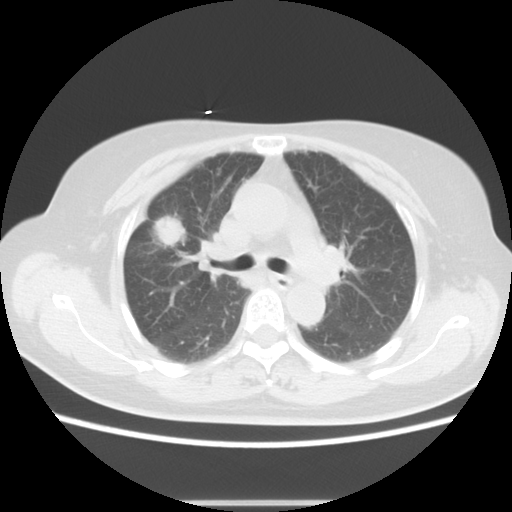
Chest CT, one axial slice; slice 8 of 14 in the series (ordered by position); 120 kVp; lung window (W 1500 / L -600 HU); 5 mm slice thickness; 512 × 512 image matrix, field of view 350 × 350 mm. Patient: female, 57 years. Case-level facts recorded for this patient, not image findings: clinical TNM (as recorded): T1c N1 M0.
Structures marked on this image (rectangle marked by the reading radiologist):
- lung tumour (recorded histology: adenocarcinoma): bounding box <154,215,185,248> (left, top, right, bottom; pixels)